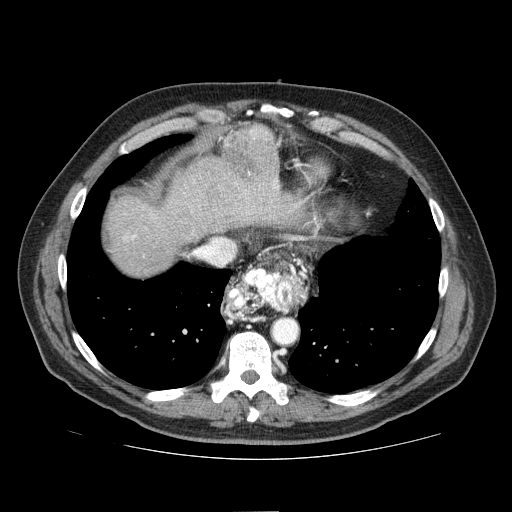
Contrast-enhanced abdominal CT (liver protocol), one axial slice; one of 2 acquisitions stored at this slice position; soft-tissue window (W 400 / L 40 HU); 2.5 mm slice thickness; 512 × 512 image matrix, field of view 400 × 400 mm. Case-level facts recorded for this patient, not image findings: diagnosis: hepatocellular carcinoma (patient treated with transarterial chemoembolisation; whether this scan precedes or follows treatment is not stated here); TNM stage (as recorded): Stage-IIIA; Child-Pugh class: A; tumour differentiation: well differentiated; tumour size: 5.6 cm.
Structures marked on this image (semi-automatic segmentation, software-assisted and operator-edited):
- liver parenchyma outside the tumour (the mass and vessels are separate outlines, so this box may not span the whole liver): bounding box <108,156,288,276> (left, top, right, bottom; pixels)
- mass: <221,124,280,188>
- liver vessels: <123,177,279,240>